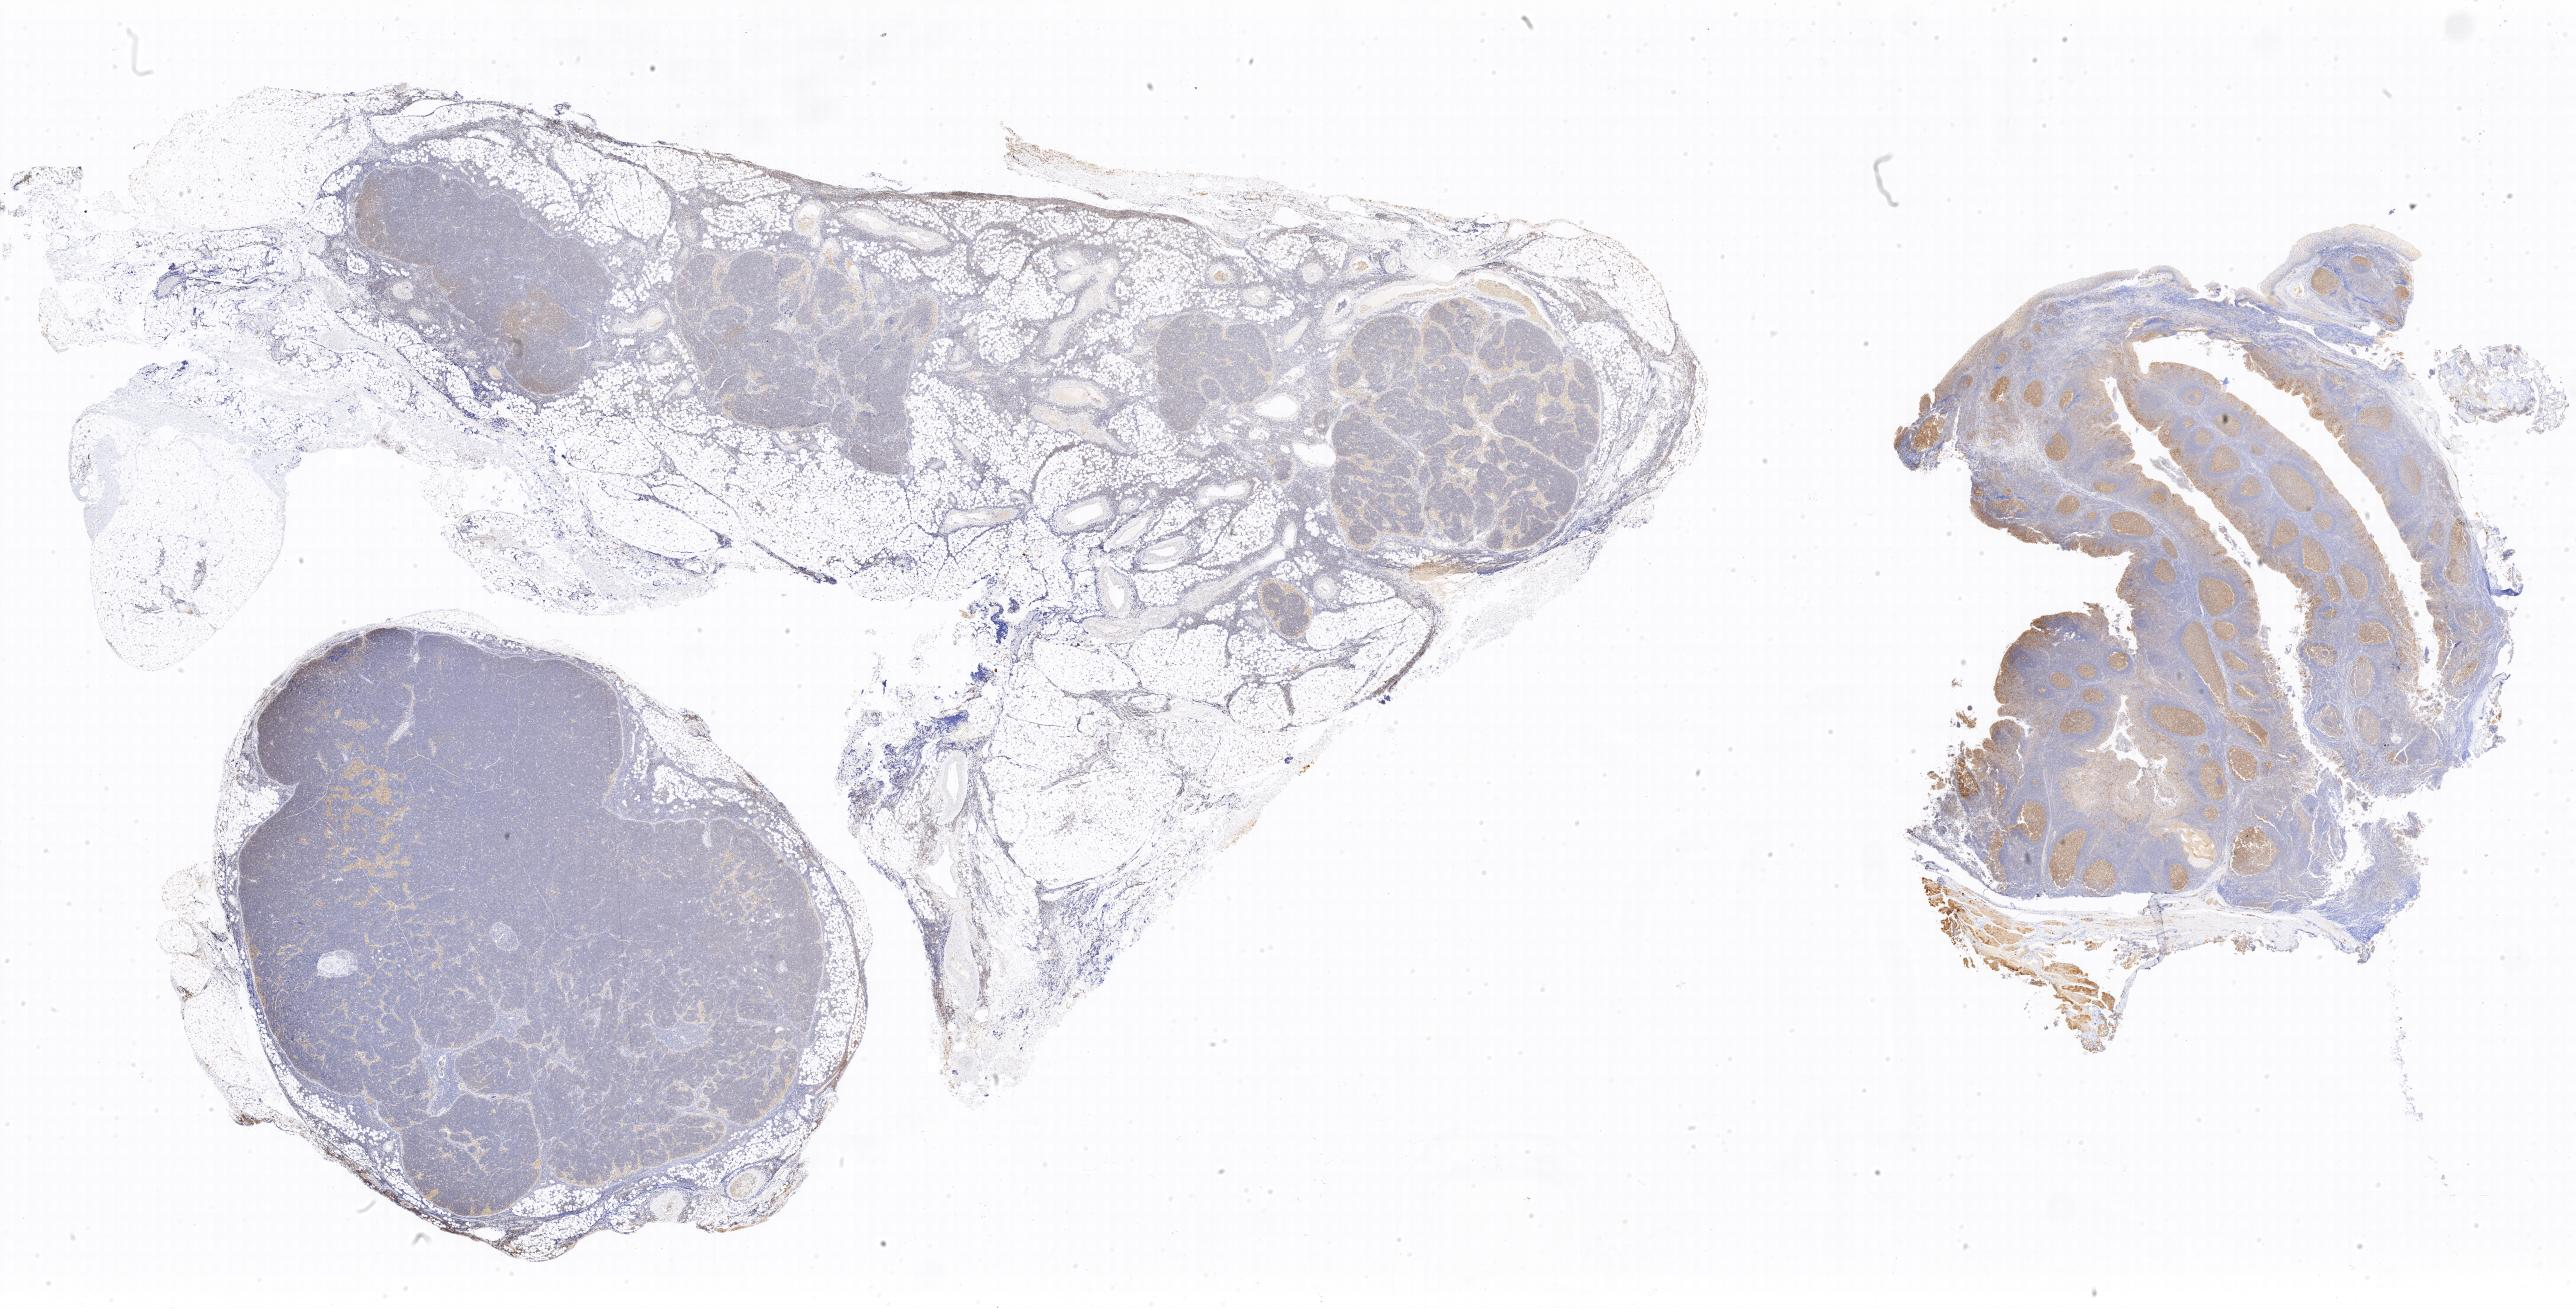
Immunohistochemistry (IHC) whole-slide image stained for BCL6, shown as a low-resolution overview of the whole scanned area, tumor tissue, anatomic site: spleen. Patient: female, aged 15.
- histologic diagnosis: Burkitt lymphoma, NOS